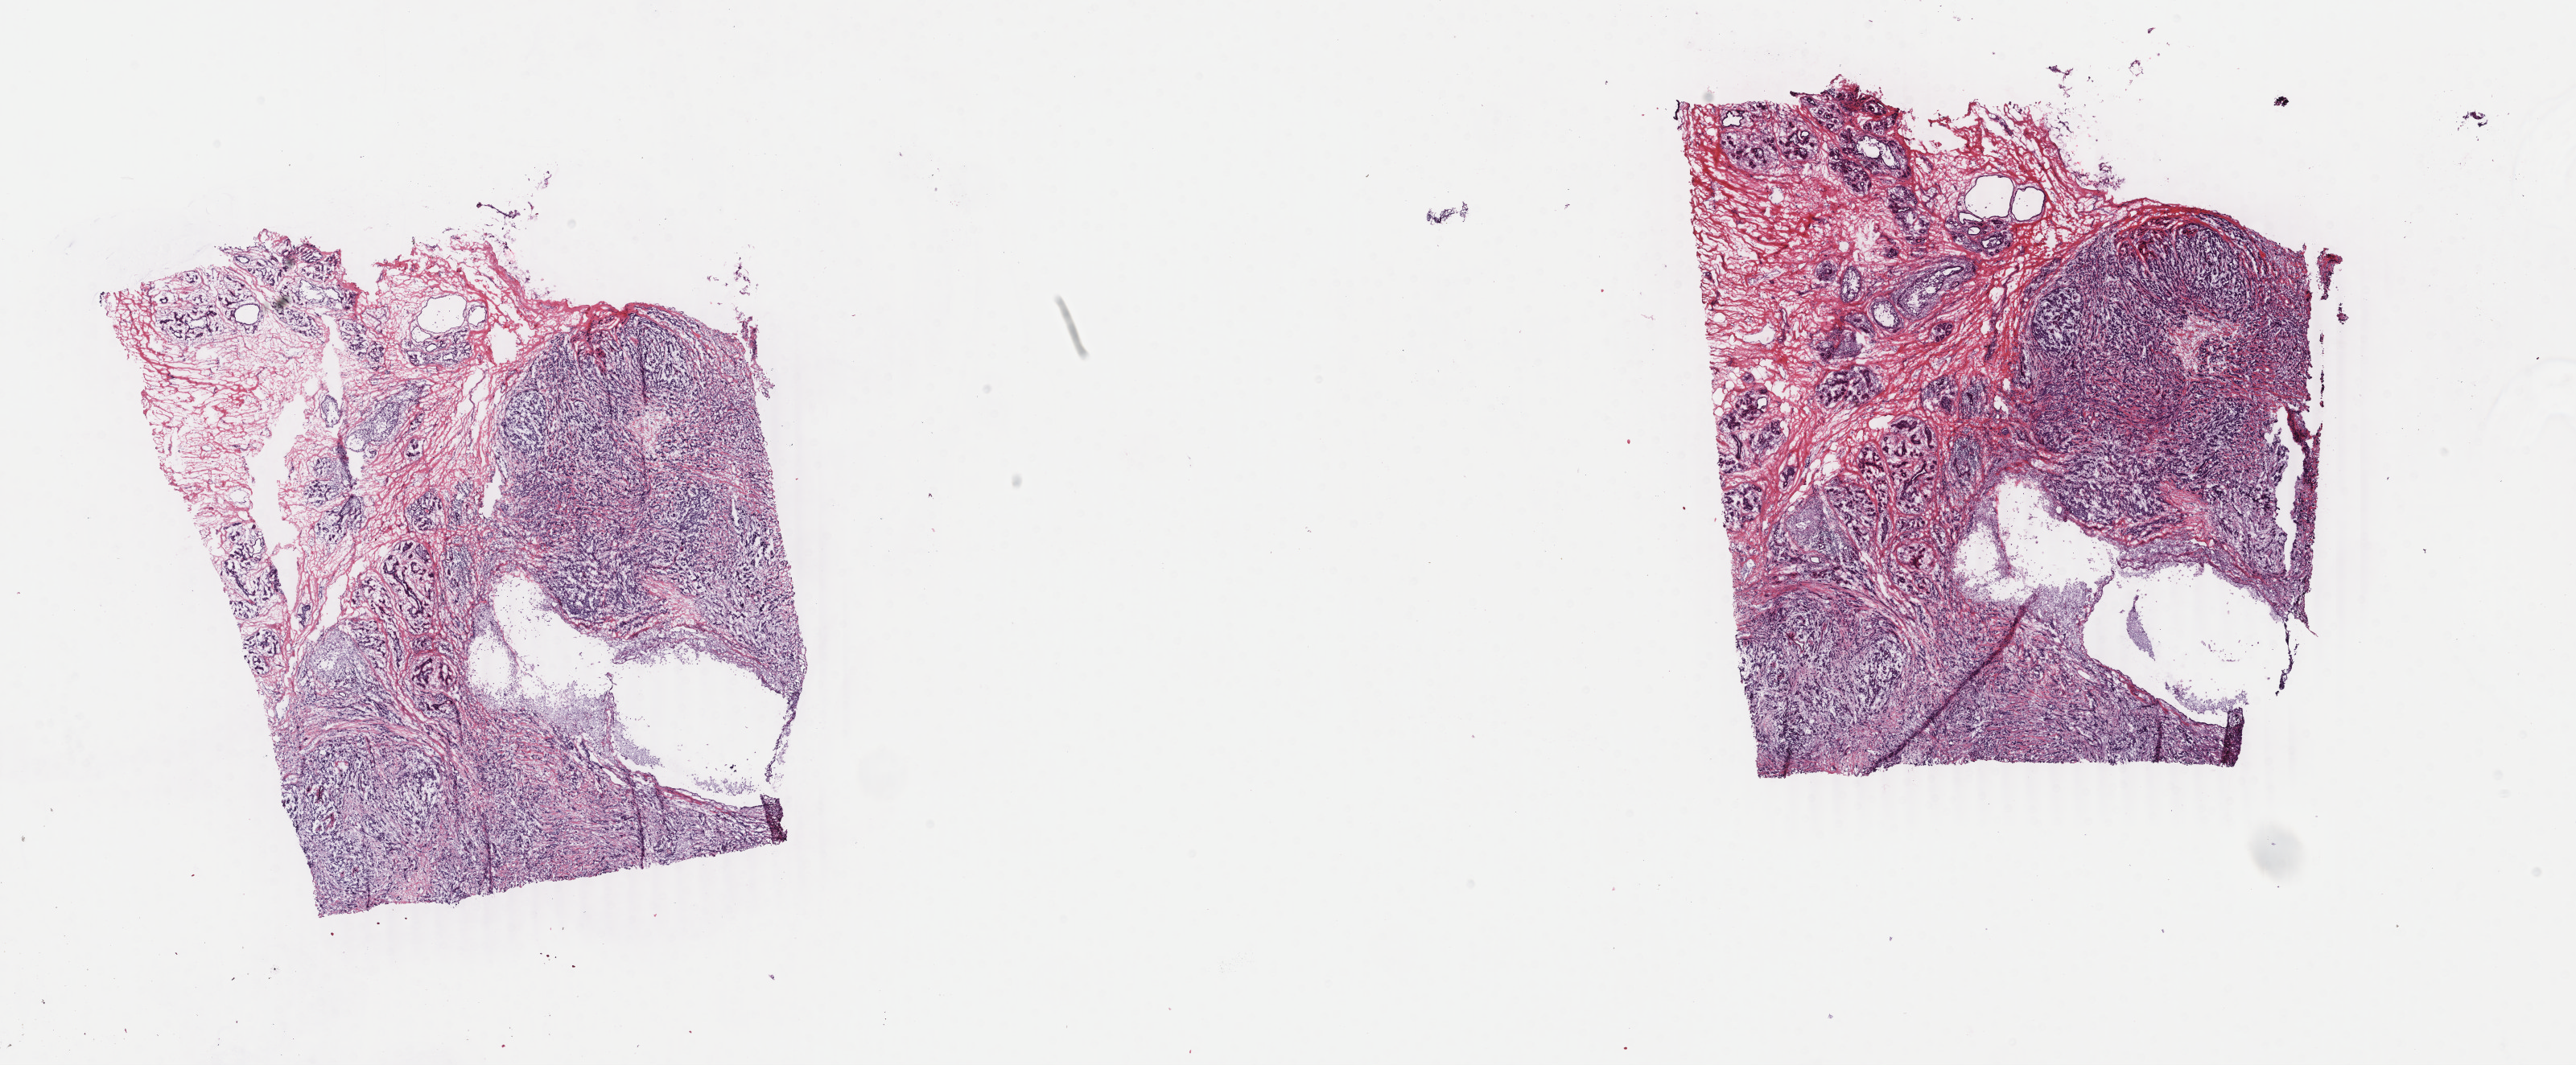
Digitized Hematoxylin and eosin (H&E) stained tissue section (whole slide) — whole scanned area (about 25.5 x 10.5 mm) shown as a low-resolution overview, frozen section, breast, primary tumour sample. Patient: female, age at initial diagnosis 51 years. Slide review estimates, as recorded: tumour cells 80%, tumour nuclei 80%, normal cells 0%, stromal cells 15%, necrosis 5%. Inflammatory infiltration, as recorded: lymphocyte infiltration 40%, monocyte infiltration 10%, neutrophil infiltration 20%.
AJCC pathologic stage: IIA. Lymph nodes positive (case pathology): 0 of 2 examined. Pathologic diagnosis: Infiltrating duct carcinoma, NOS.